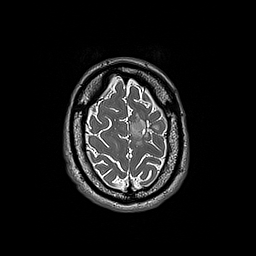
Brain MRI from a brain-tumour surgery series, one axial slice; slice 43 of 192 in the series (ordered by position); 256 × 256 image matrix, field of view 250 × 250 mm. From the clinical record (not read from this slice): histopathology: Oligodendroglioma; WHO grade: 3; IDH mutation: yes; tumour location: Left Frontal.
Annotated regions visible in this slice (expert manual segmentation):
- tumour: bounding box <130,116,159,148> (left, top, right, bottom; pixels)